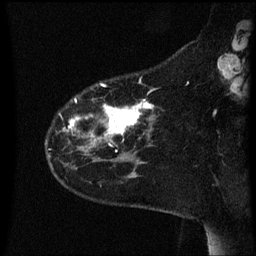
Breast MRI (dynamic contrast-enhanced), one sagittal slice; position 14 of 60 along the scan axis; dynamic contrast-enhanced series, image 2 of 3 at this slice position (ordered by acquisition); 1.5 T; TE 4.2 ms, TR 8.4 ms; 2.2 mm slice thickness; 256 × 256 image matrix, field of view 200 × 200 mm. Patient: female, 35 years. From the clinical record (not read from this slice): setting: breast cancer imaged before/during neoadjuvant chemotherapy; receptor status: HER2-positive.
Structures marked on this image (semi-automatically segmented with operator editing):
- analysis volume of interest (the breast-tissue region the enhancement analysis was run in; not a lesion): bounding box [x1, y1, x2, y2] px = [47, 84, 164, 163]
- tumour enhancement mask (voxels above the 70 % enhancement threshold inside the analysis volume of interest): [70, 100, 155, 137]